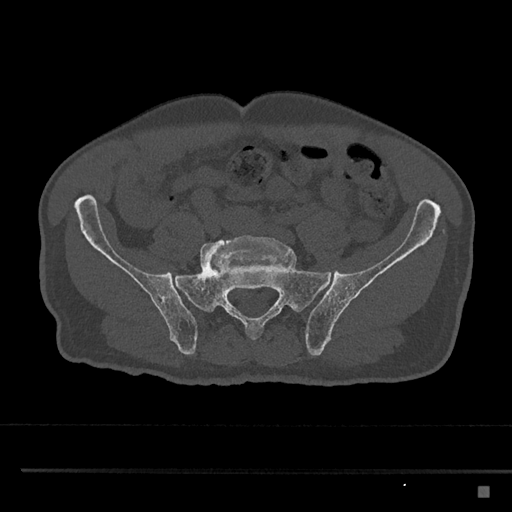
CT including the spine, one axial slice; slice 543 of 797 in the series (ordered by position); reconstruction kernel Br40s/3; bone window (W 1800 / L 400 HU); 512 × 512 image matrix, field of view 391 × 391 mm. Patient: male, 59 years. Case-level facts recorded for this patient, not image findings: primary cancer: prostate.
Structures marked on this image (semi-automatic segmentation, software-assisted and operator-edited):
- L5 vertebra: bounding box <200,235,292,273> (left, top, right, bottom; pixels)